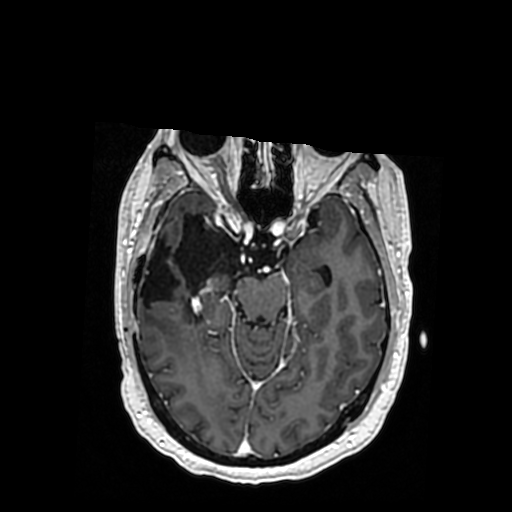
Brain MRI from a brain-tumour surgery series, one axial slice. Slice 219 of 364 in the series (ordered by position). T1-weighted post-contrast. 512 × 512 image matrix, field of view 260 × 260 mm. From the clinical record (not read from this slice): histopathology: Oligodendroglioma; WHO grade: 3; IDH mutation: yes; tumour location: Right Posterior Temporal Inferior Parietal.
Structures marked on this image (expert manual segmentation):
- previous resection cavity: bounding box (x1, y1, x2, y2) in pixels: (140, 215, 240, 319)